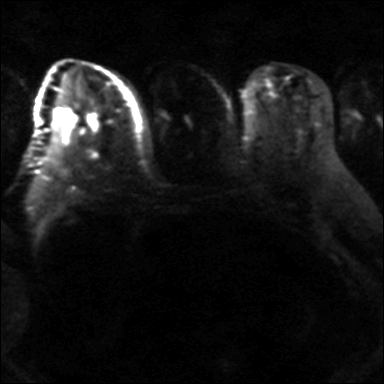
Breast MRI, one axial slice. Slice 19 of 36 in the series (ordered by position). Diffusion-weighted series; image 2 of 4 stored at this slice position (different b-values; order by instance number). 3 T. 4 mm slice thickness. 384 × 384 image matrix, field of view 320 × 320 mm. Female patient.
Outlined on this slice (outlined manually by an expert reader):
- tumour on diffusion-weighted imaging: box from (x=66, y=123) to (x=76, y=135) px